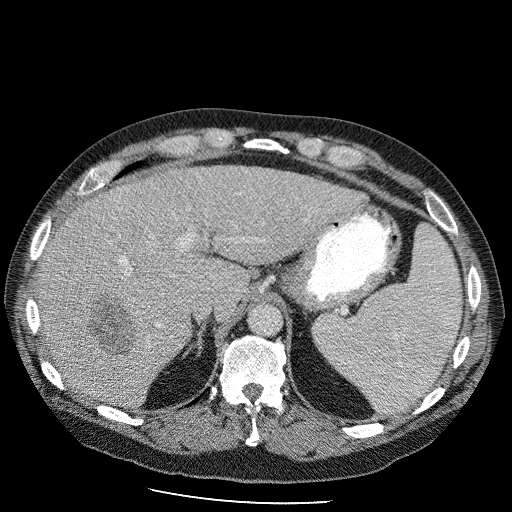
Contrast-enhanced abdominal CT (liver protocol), one axial slice. Position 73 of 98 along the scan axis. Reconstruction kernel STANDARD. 120 kVp. Soft-tissue window (W 400 / L 40 HU). 2.5 mm slice thickness. 512 × 512 image matrix, field of view 400 × 400 mm. From the clinical record (not read from this slice): diagnosis: hepatocellular carcinoma (patient treated with transarterial chemoembolisation; whether this scan precedes or follows treatment is not stated here); TNM stage (as recorded): Stage-II; Child-Pugh class: B; tumour differentiation: moderately differentiated.
Annotated regions visible in this slice (semi-automatically segmented with operator editing):
- liver parenchyma outside the tumour (the mass and vessels are separate outlines, so this box may not span the whole liver): bounding box (x1, y1, x2, y2) in pixels: (36, 164, 363, 408)
- mass: (75, 283, 153, 362)
- liver vessels: (120, 228, 209, 325)